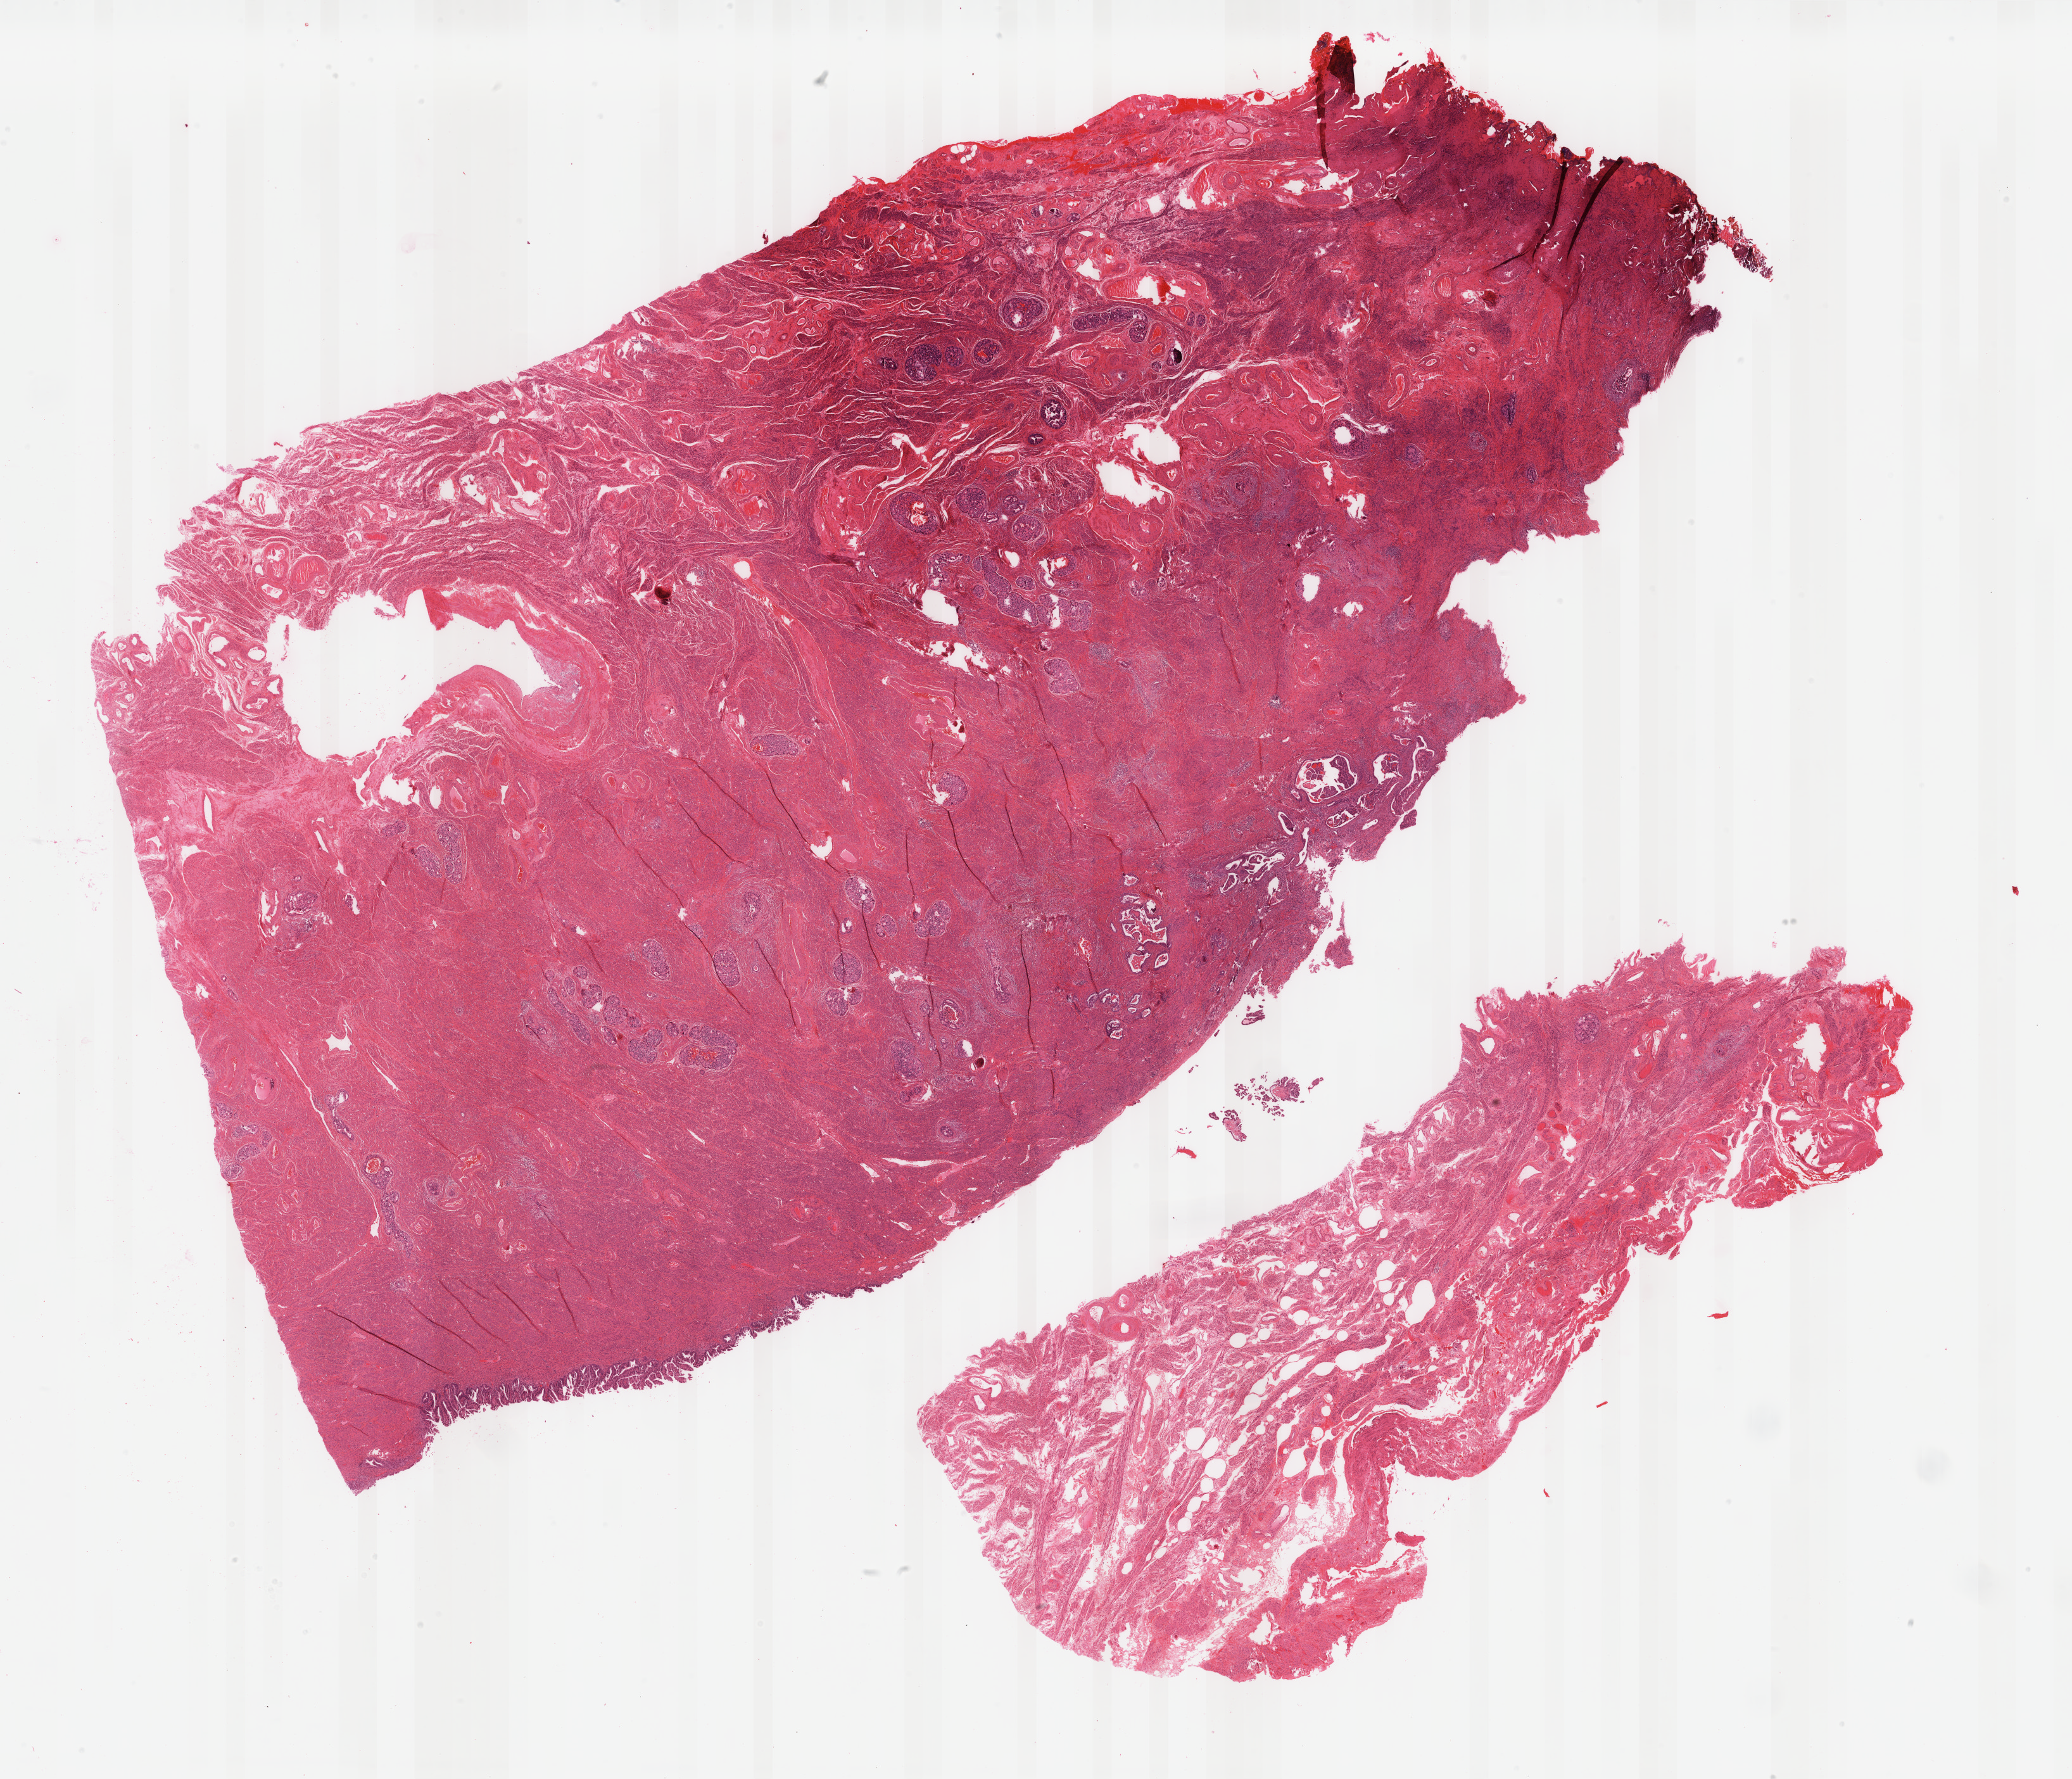
Digitized H&E tissue section (whole slide) — low-resolution overview of the scanned area, about 26.0 x 22.3 mm; formalin-fixed paraffin-embedded (FFPE) diagnostic section; uterus, primary tumour sample. Female patient; age at initial diagnosis 63 years. Histologic grade: G3 (poorly differentiated).
* histologic diagnosis: Serous cystadenocarcinoma, NOS (endometrium)
* FIGO stage: IIIA